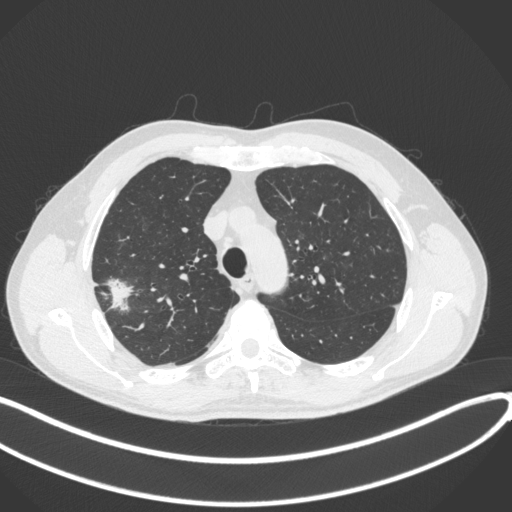
Chest CT, one axial slice. Slice 315 of 381 in the series (ordered by position). Reconstruction kernel B31f. 120 kVp. Lung window (W 1500 / L -600 HU). 1 mm slice thickness. 512 × 512 image matrix, field of view 400 × 400 mm. Patient: male, 62 years. Case-level facts recorded for this patient, not image findings: clinical TNM (as recorded): T1c N0 M0; histopathological grade: G2-3.
Annotated regions visible in this slice (rectangle marked by the reading radiologist):
- lung tumour (recorded histology: adenocarcinoma): box from (x=103, y=276) to (x=136, y=313) px